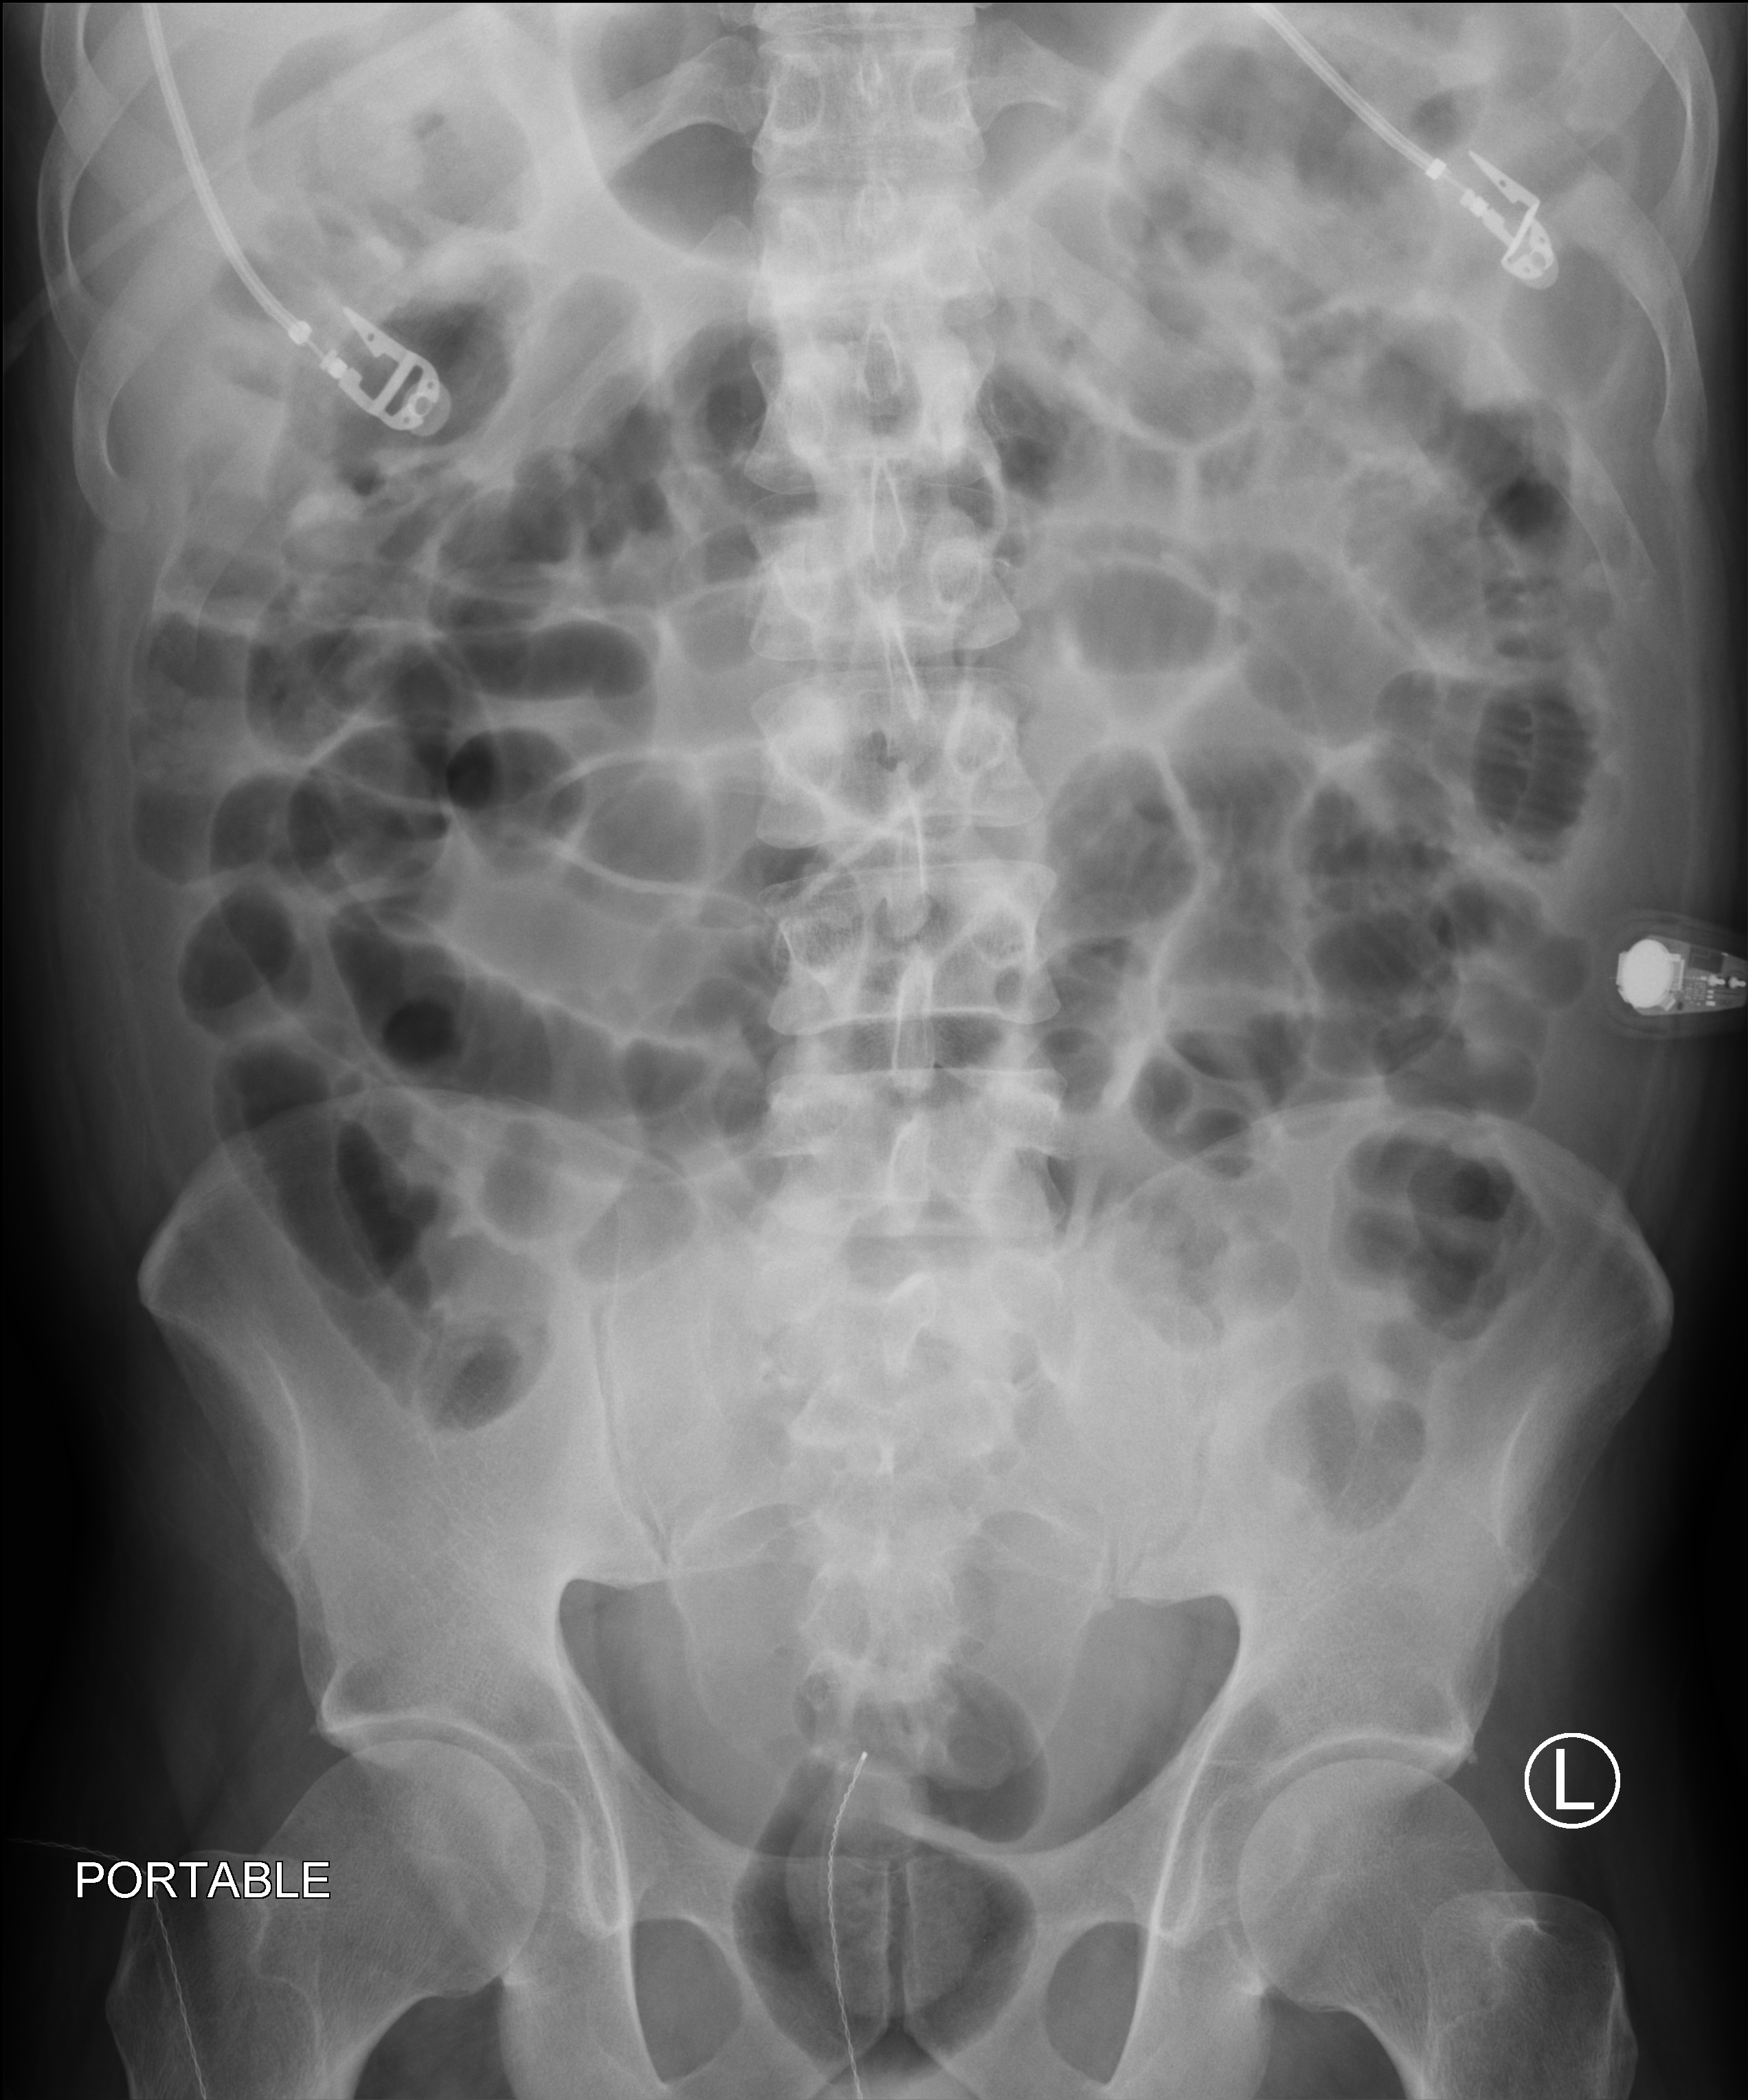
Abdomen X-ray (portable), anteroposterior (AP) projection. Male patient hospitalised with COVID-19, age 18–59 years.
From the hospital-stay record, not from the radiograph (when in the stay this image was taken is not recorded): length of hospital stay: 44 days.